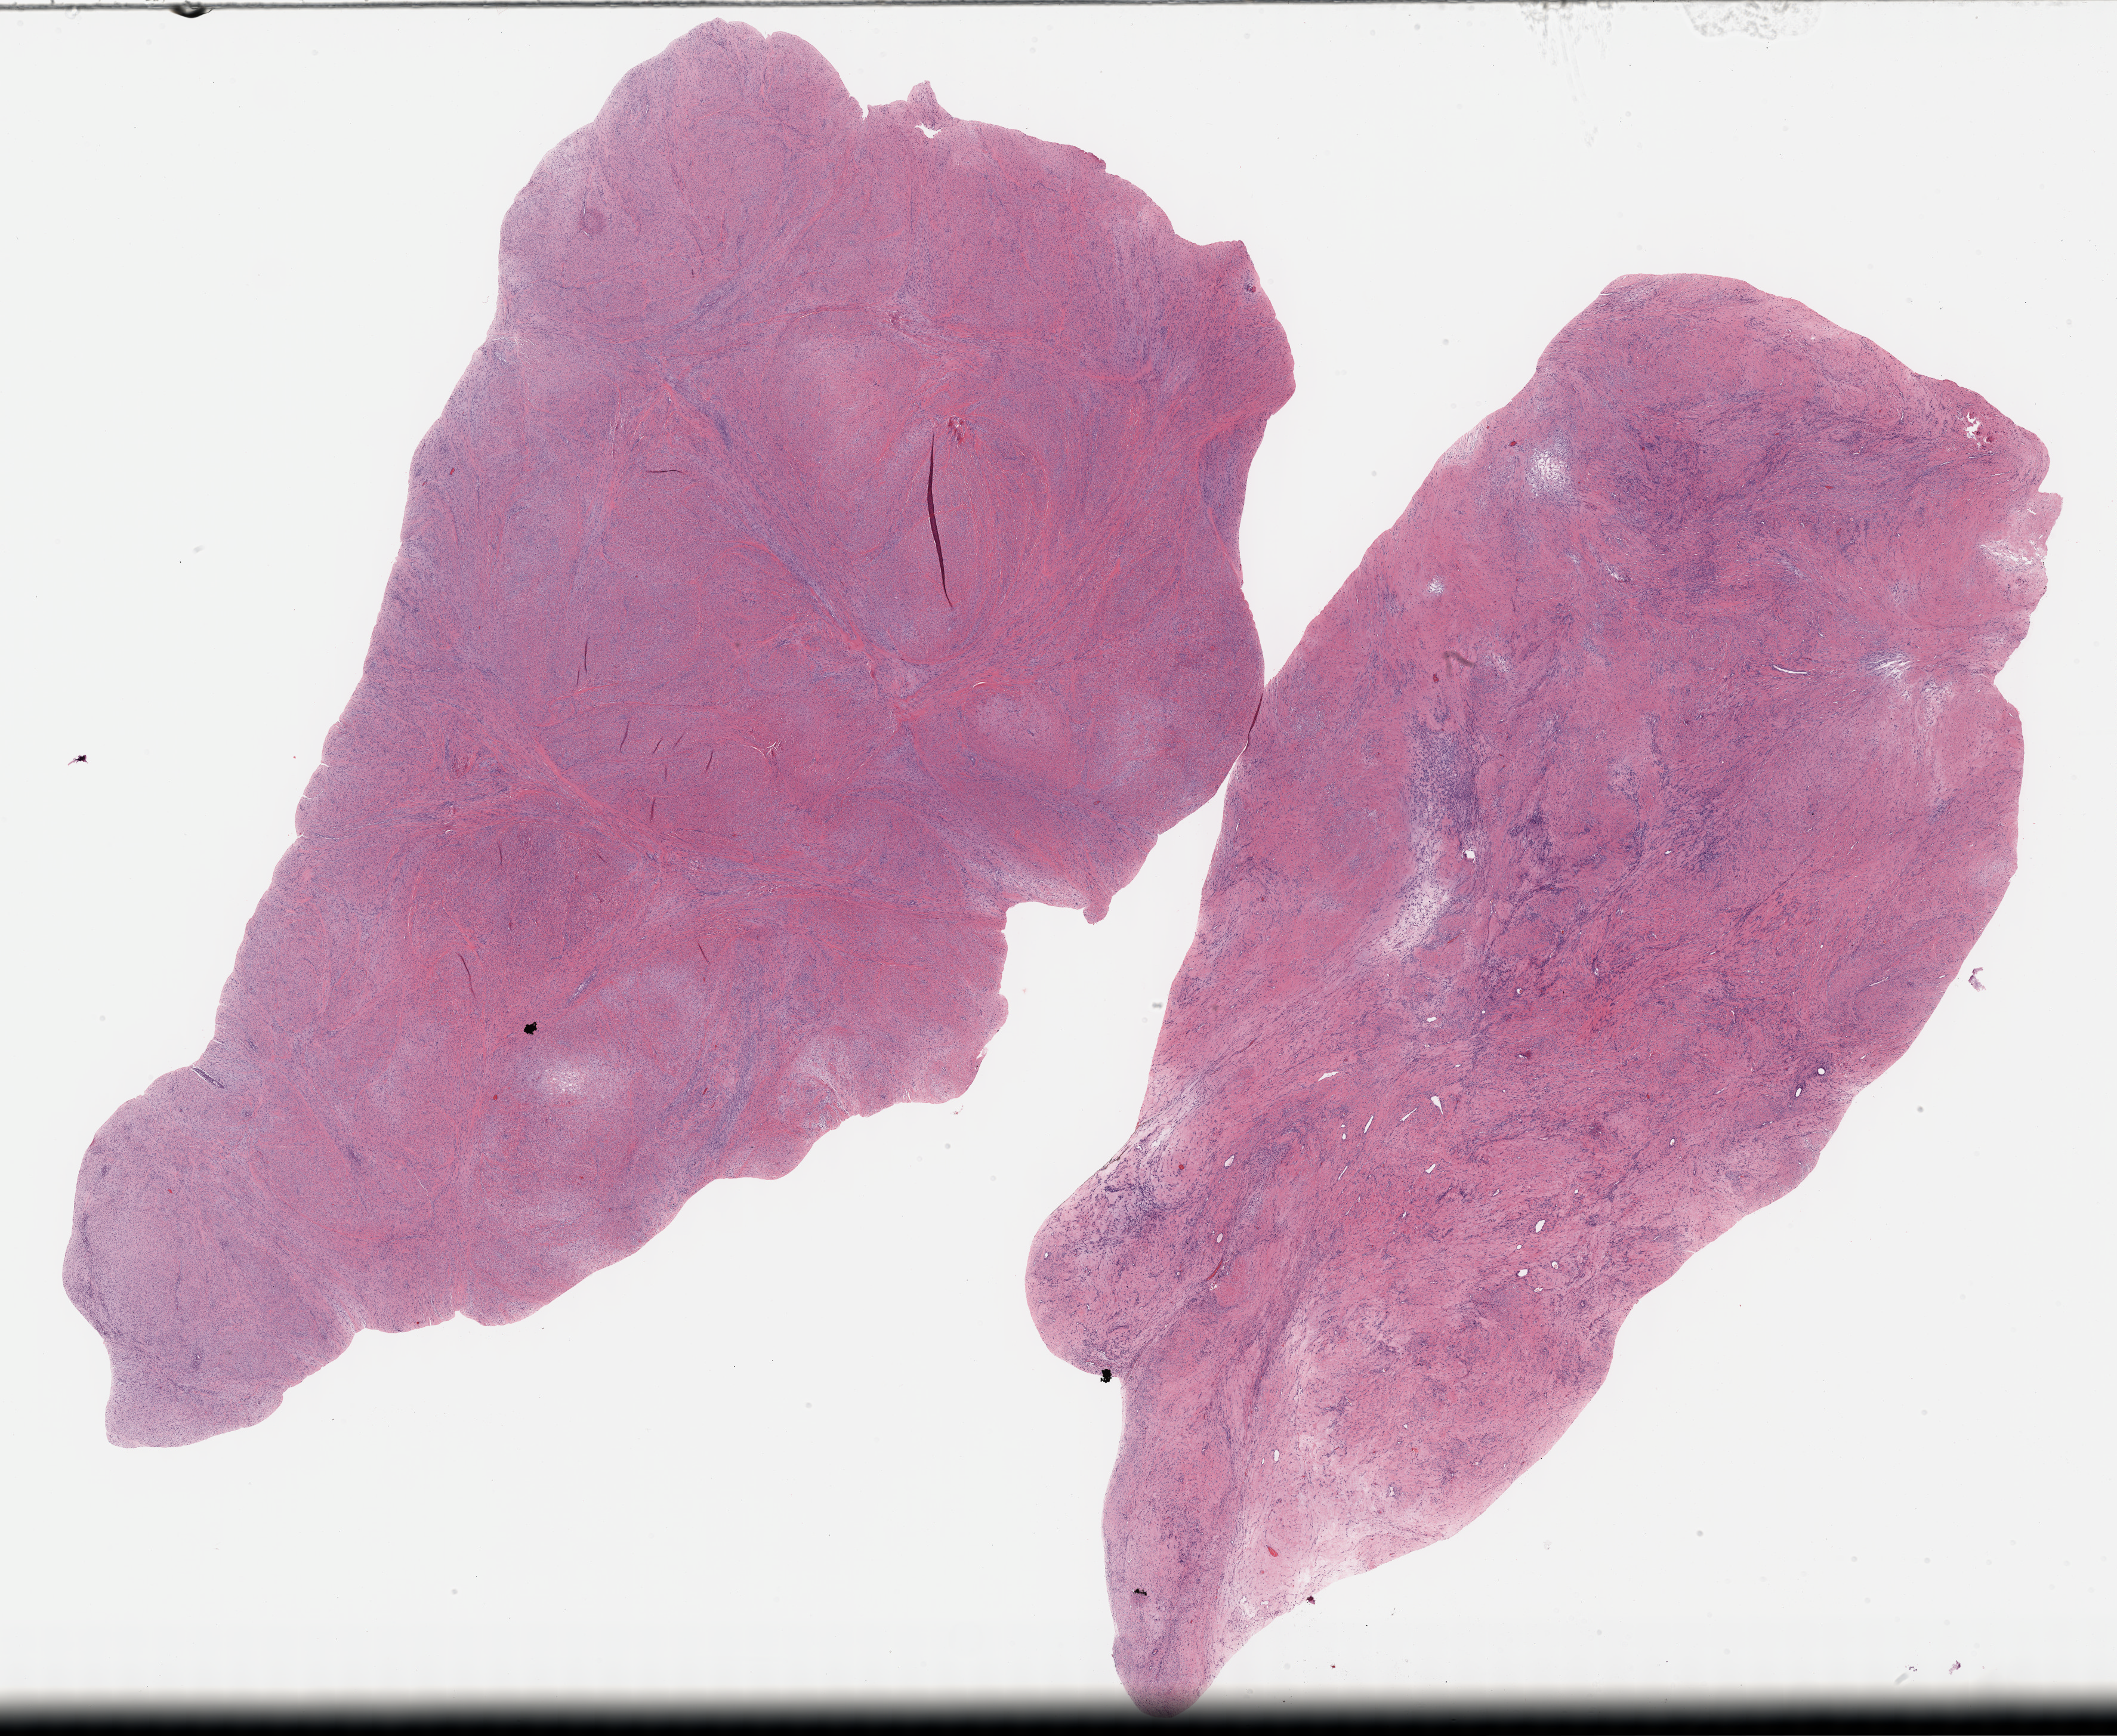
Whole-slide histology image, Hematoxylin and eosin (H&E) stained, shown as a low-resolution overview of the whole scanned area (about 28.7 x 23.5 mm, from a 40x scan); FFPE section; sample: primary tumour, other and unspecified male genital organs. Patient: male, age at initial diagnosis 51 years.
Pathologic diagnosis: Dedifferentiated liposarcoma (spermatic cord).